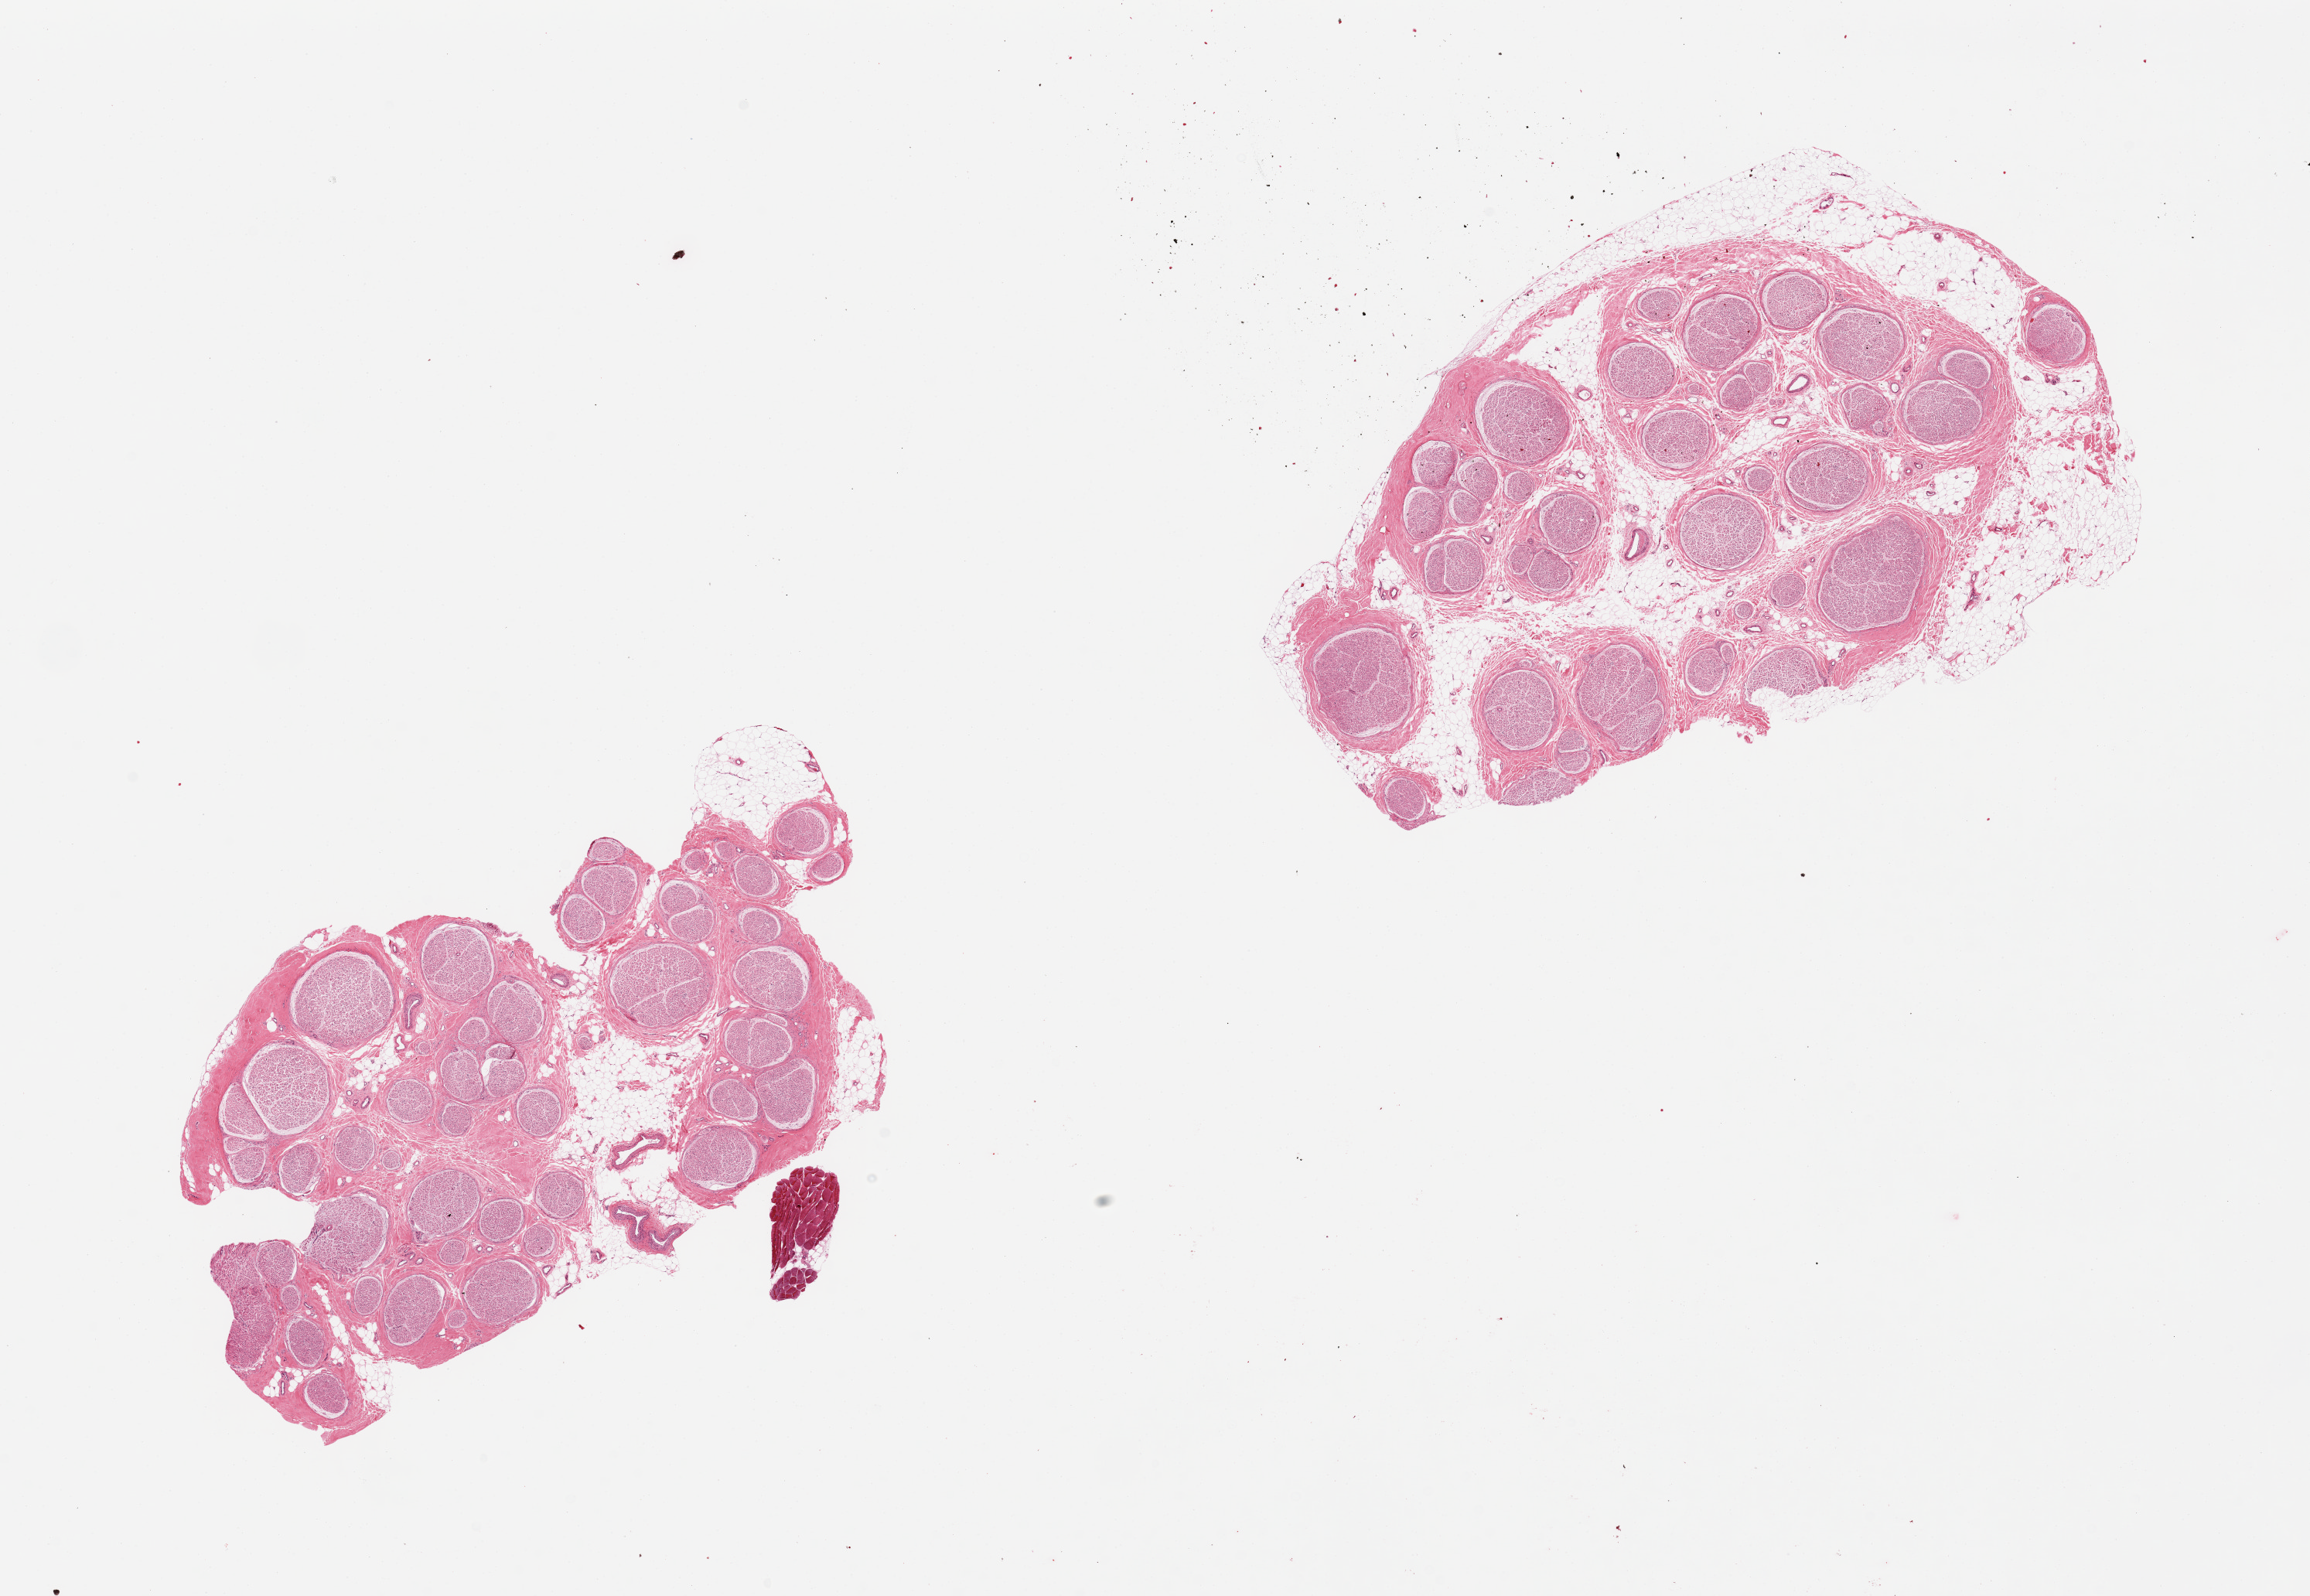
Digitized haematoxylin and eosin-stained section, a low-resolution overview of the entire scanned area, about 23.6 x 16.3 mm (acquisition: 20x scan); PAXgene-fixed paraffin-embedded (PFPE) section; section of tibial nerve (target tissue); tissue donor sample. Donor: male.
Reviewer comment on this tissue sample: 2 pieces, discontinous rim of adherent fat up to ~1.5mm.